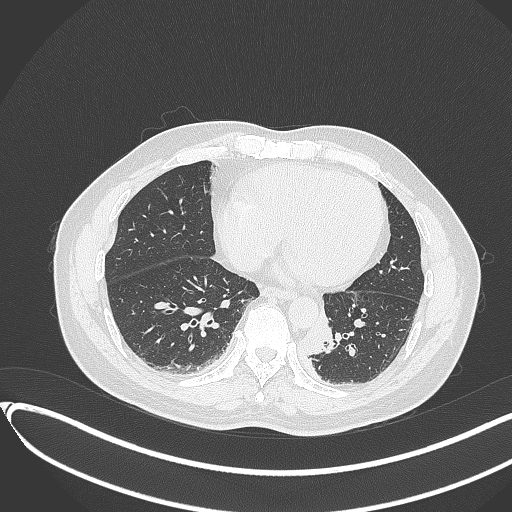
Chest CT, one axial slice. Slice 112 of 417 in the series (ordered by position). Reconstruction kernel B70f. 120 kVp. Lung window (W 1500 / L -600 HU). 1 mm slice thickness. 512 × 512 image matrix, field of view 400 × 400 mm. Patient: male, 54 years. From the clinical record (not read from this slice): clinical TNM (as recorded): T3 N0 M0.
Annotated regions visible in this slice (bounding box drawn by a radiologist):
- lung tumour (recorded histology: squamous cell carcinoma): bounding box <306,307,336,358> (left, top, right, bottom; pixels)